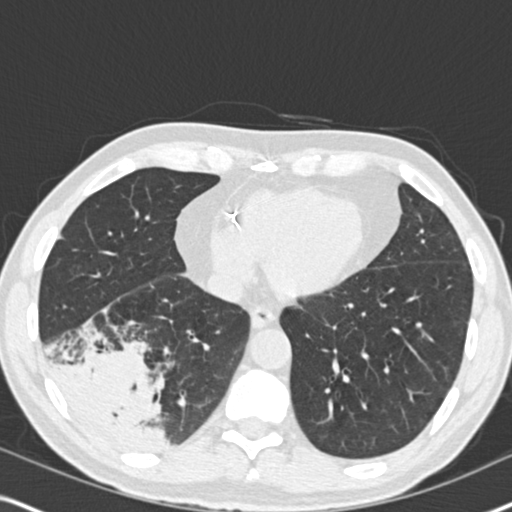
Low-dose screening chest CT, axial slice, second annual screen, lung window (W 1500 / L -600 HU), slice 116 of 182 in the series. Male participant, aged 61 years at enrolment. Current smoker at enrolment.
Expert-annotated lung lesion, bounding box <39,310,186,461> (left, top, right, bottom; pixels). Reader record for this screening exam (exam-level; its link to the box is not recorded): non-calcified nodule or mass ≥4 mm, right lower lobe, 90 × 80 mm, soft tissue attenuation, pre-existing on the prior screen: yes; interval growth: yes.